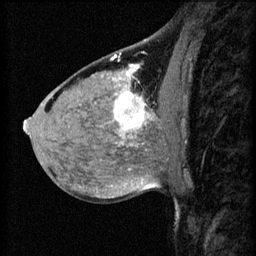
Breast MRI (dynamic contrast-enhanced), one sagittal slice. 3 images stored at this slice position (order not interpretable as contrast timing). 1.5 T. TE 4.2 ms, TR 8.2 ms. 2.2 mm slice thickness. 256 × 256 image matrix, field of view 180 × 180 mm. Patient: female, 40 years.
Outlined on this slice (semi-automatically segmented with operator editing):
- analysis volume of interest (the breast-tissue region the enhancement analysis was run in; not a lesion): bounding box [x1, y1, x2, y2] px = [108, 82, 175, 139]
- tumour enhancement mask (voxels above the 70 % enhancement threshold inside the analysis volume of interest): [114, 92, 153, 133]